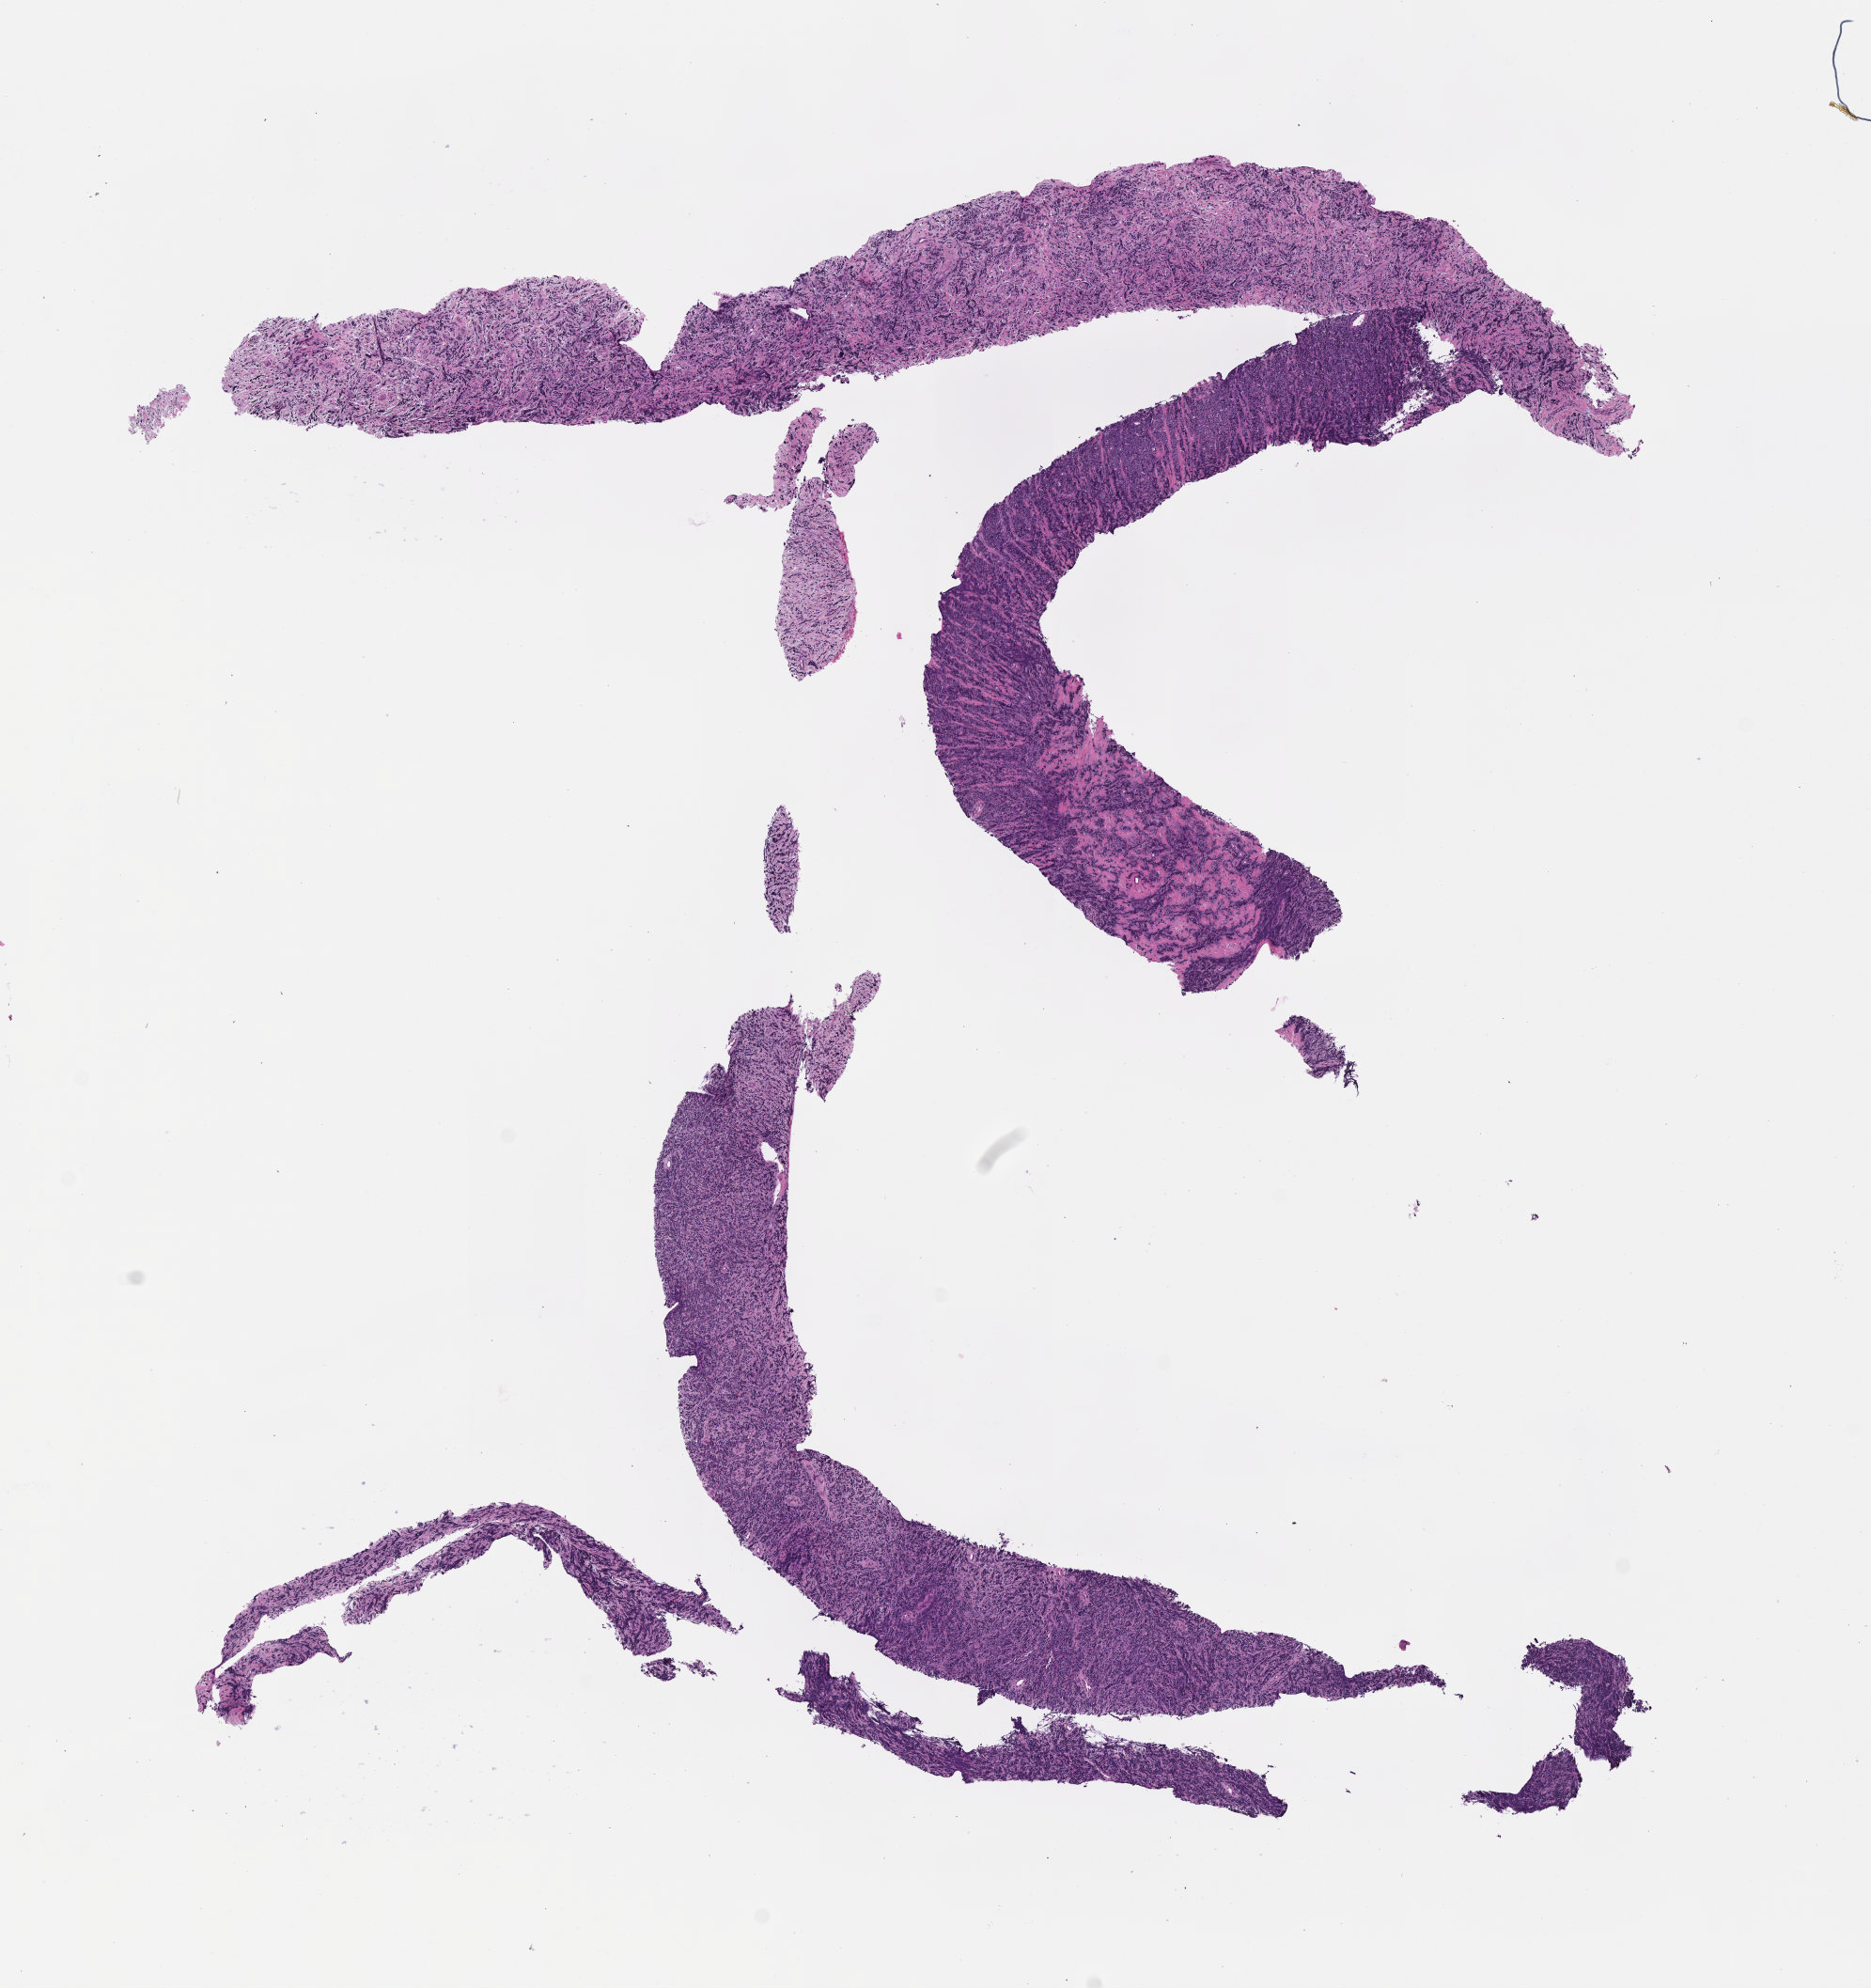
Digitized hematoxylin and eosin (H&E)-stained section — shown as a low-resolution overview of the whole scanned area (about 8.1 x 8.6 mm); specimen: tumor tissue; anatomic site: pleura. Male patient; age at initial diagnosis 2 years.
Histologic diagnosis: Diffuse large B-cell lymphoma, NOS.